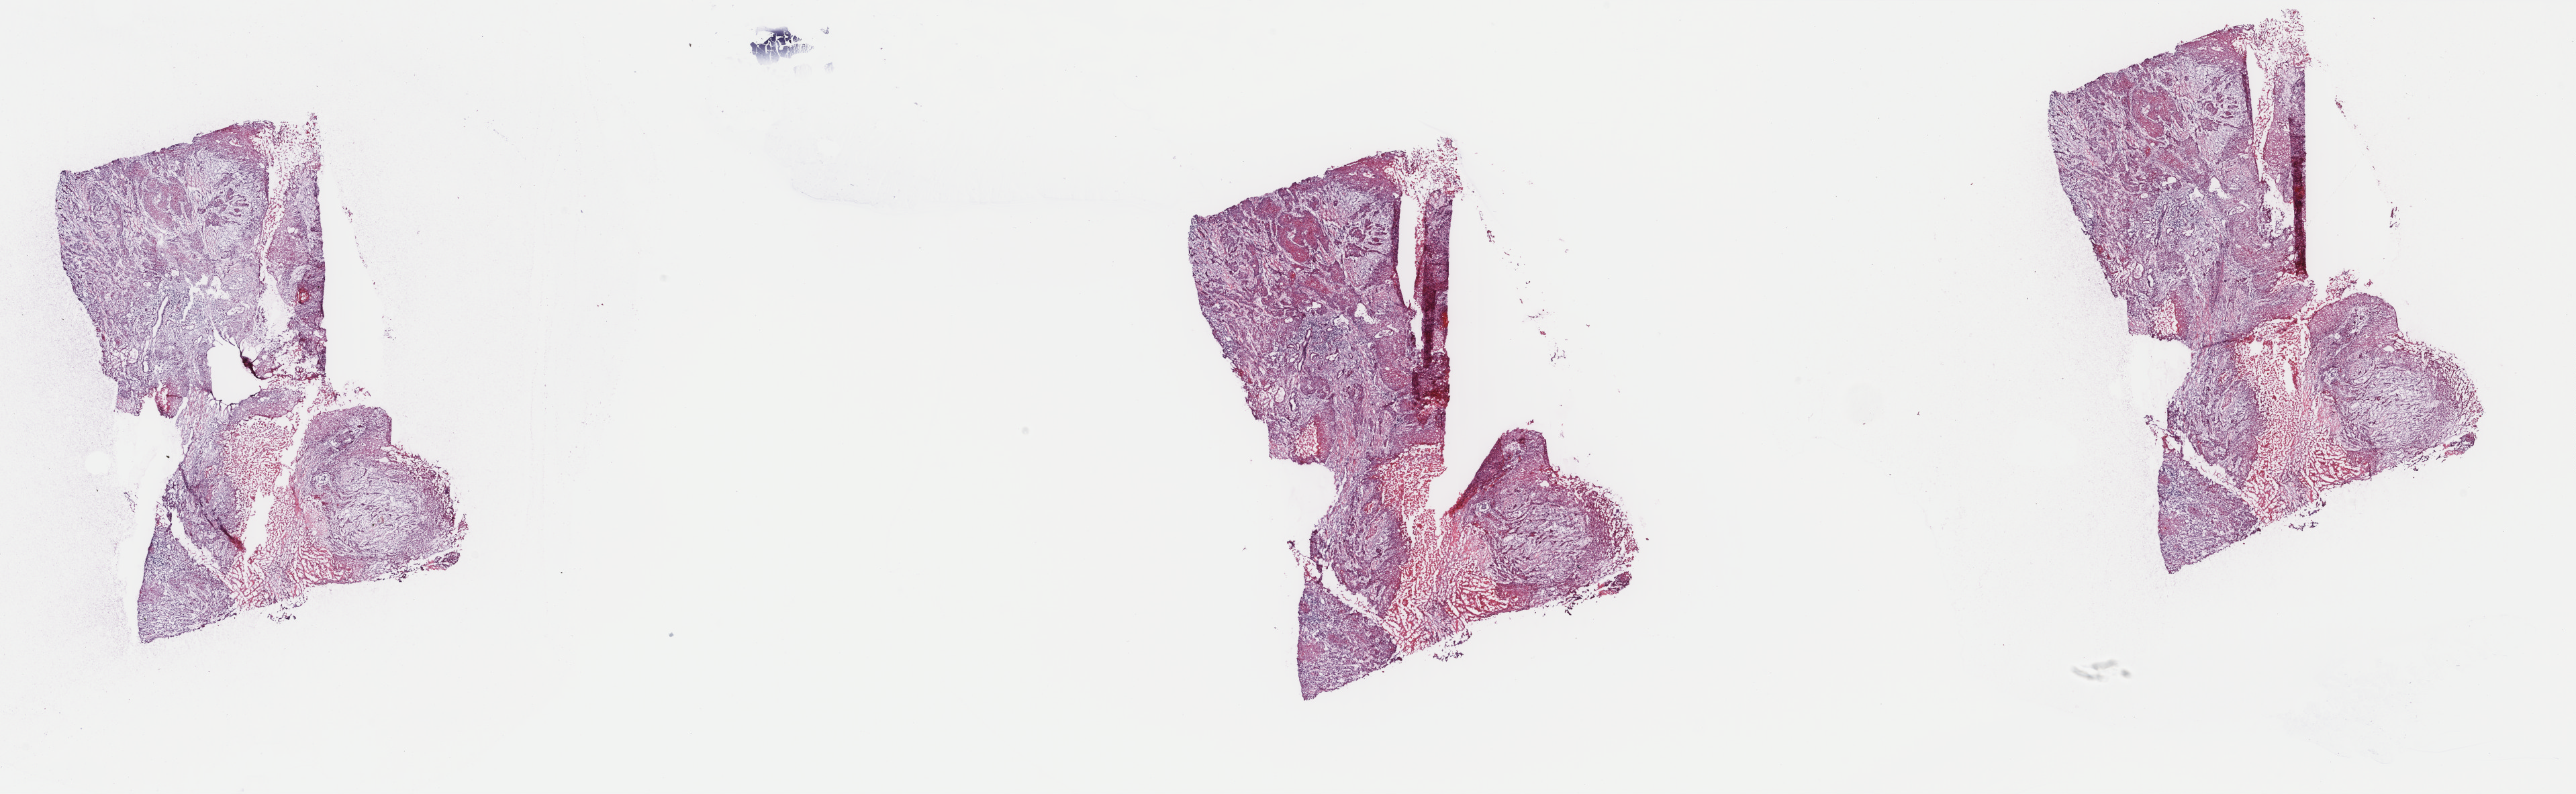
Whole-slide histology image, H&E — a low-resolution overview of the entire scanned area, about 30.5 x 9.4 mm (from a 40x scan), frozen section from the top of the tissue portion, head and neck, primary tumour sample. Male patient; age at initial diagnosis 62 years. Histologic grade: G2 (moderately differentiated). Pathologist review of this section (percent, as recorded): tumour cells 60%, tumour nuclei 70%, normal cells 10%, stromal cells 30%, necrosis 0%. Inflammatory infiltration, as recorded: lymphocyte infiltration 0%, monocyte infiltration 0%, neutrophil infiltration 0%.
* AJCC pathologic stage: IVA (7th edition)
* pathologic diagnosis: Squamous cell carcinoma, NOS (larynx, NOS)
* laterality: midline